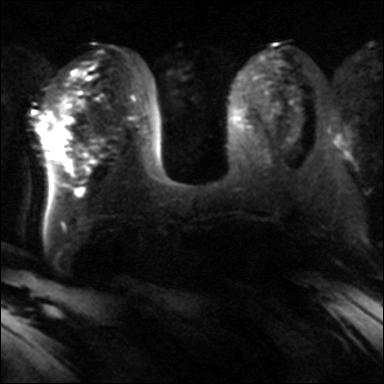
Breast MRI, one axial slice; position 16 of 40 along the scan axis; diffusion-weighted series; image 2 of 4 stored at this slice position (different b-values; order by instance number); 3 T; 384 × 384 image matrix, field of view 320 × 320 mm. Female patient.
Structures marked on this image (manually delineated by an expert):
- tumour on diffusion-weighted imaging: bounding box [x1, y1, x2, y2] px = [47, 126, 69, 147]